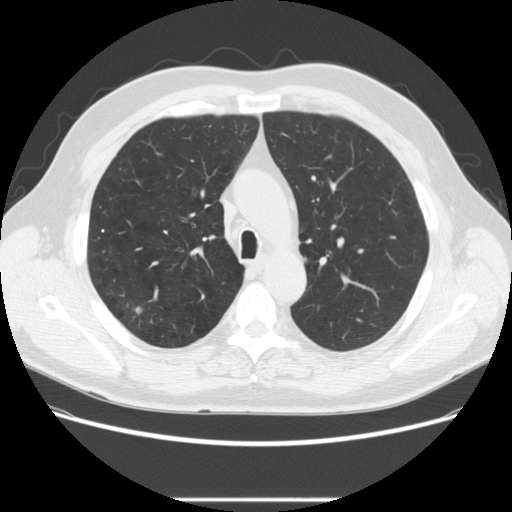
Low-dose screening chest CT, axial slice; baseline annual screen; lung window (W 1500 / L -600 HU); standard (soft-tissue) reconstruction kernel (STANDARD); slice 80 of 270 in the series; 512 × 512 image matrix. Male participant, aged 64 years at enrolment. Former smoker at enrolment.
Lesion marked by an expert reader, bounding box [x1, y1, x2, y2] px = [115, 299, 151, 327]. The screening reader recorded 2 non-calcified nodules or masses ≥4 mm on this exam; which of them this box marks is not recorded.